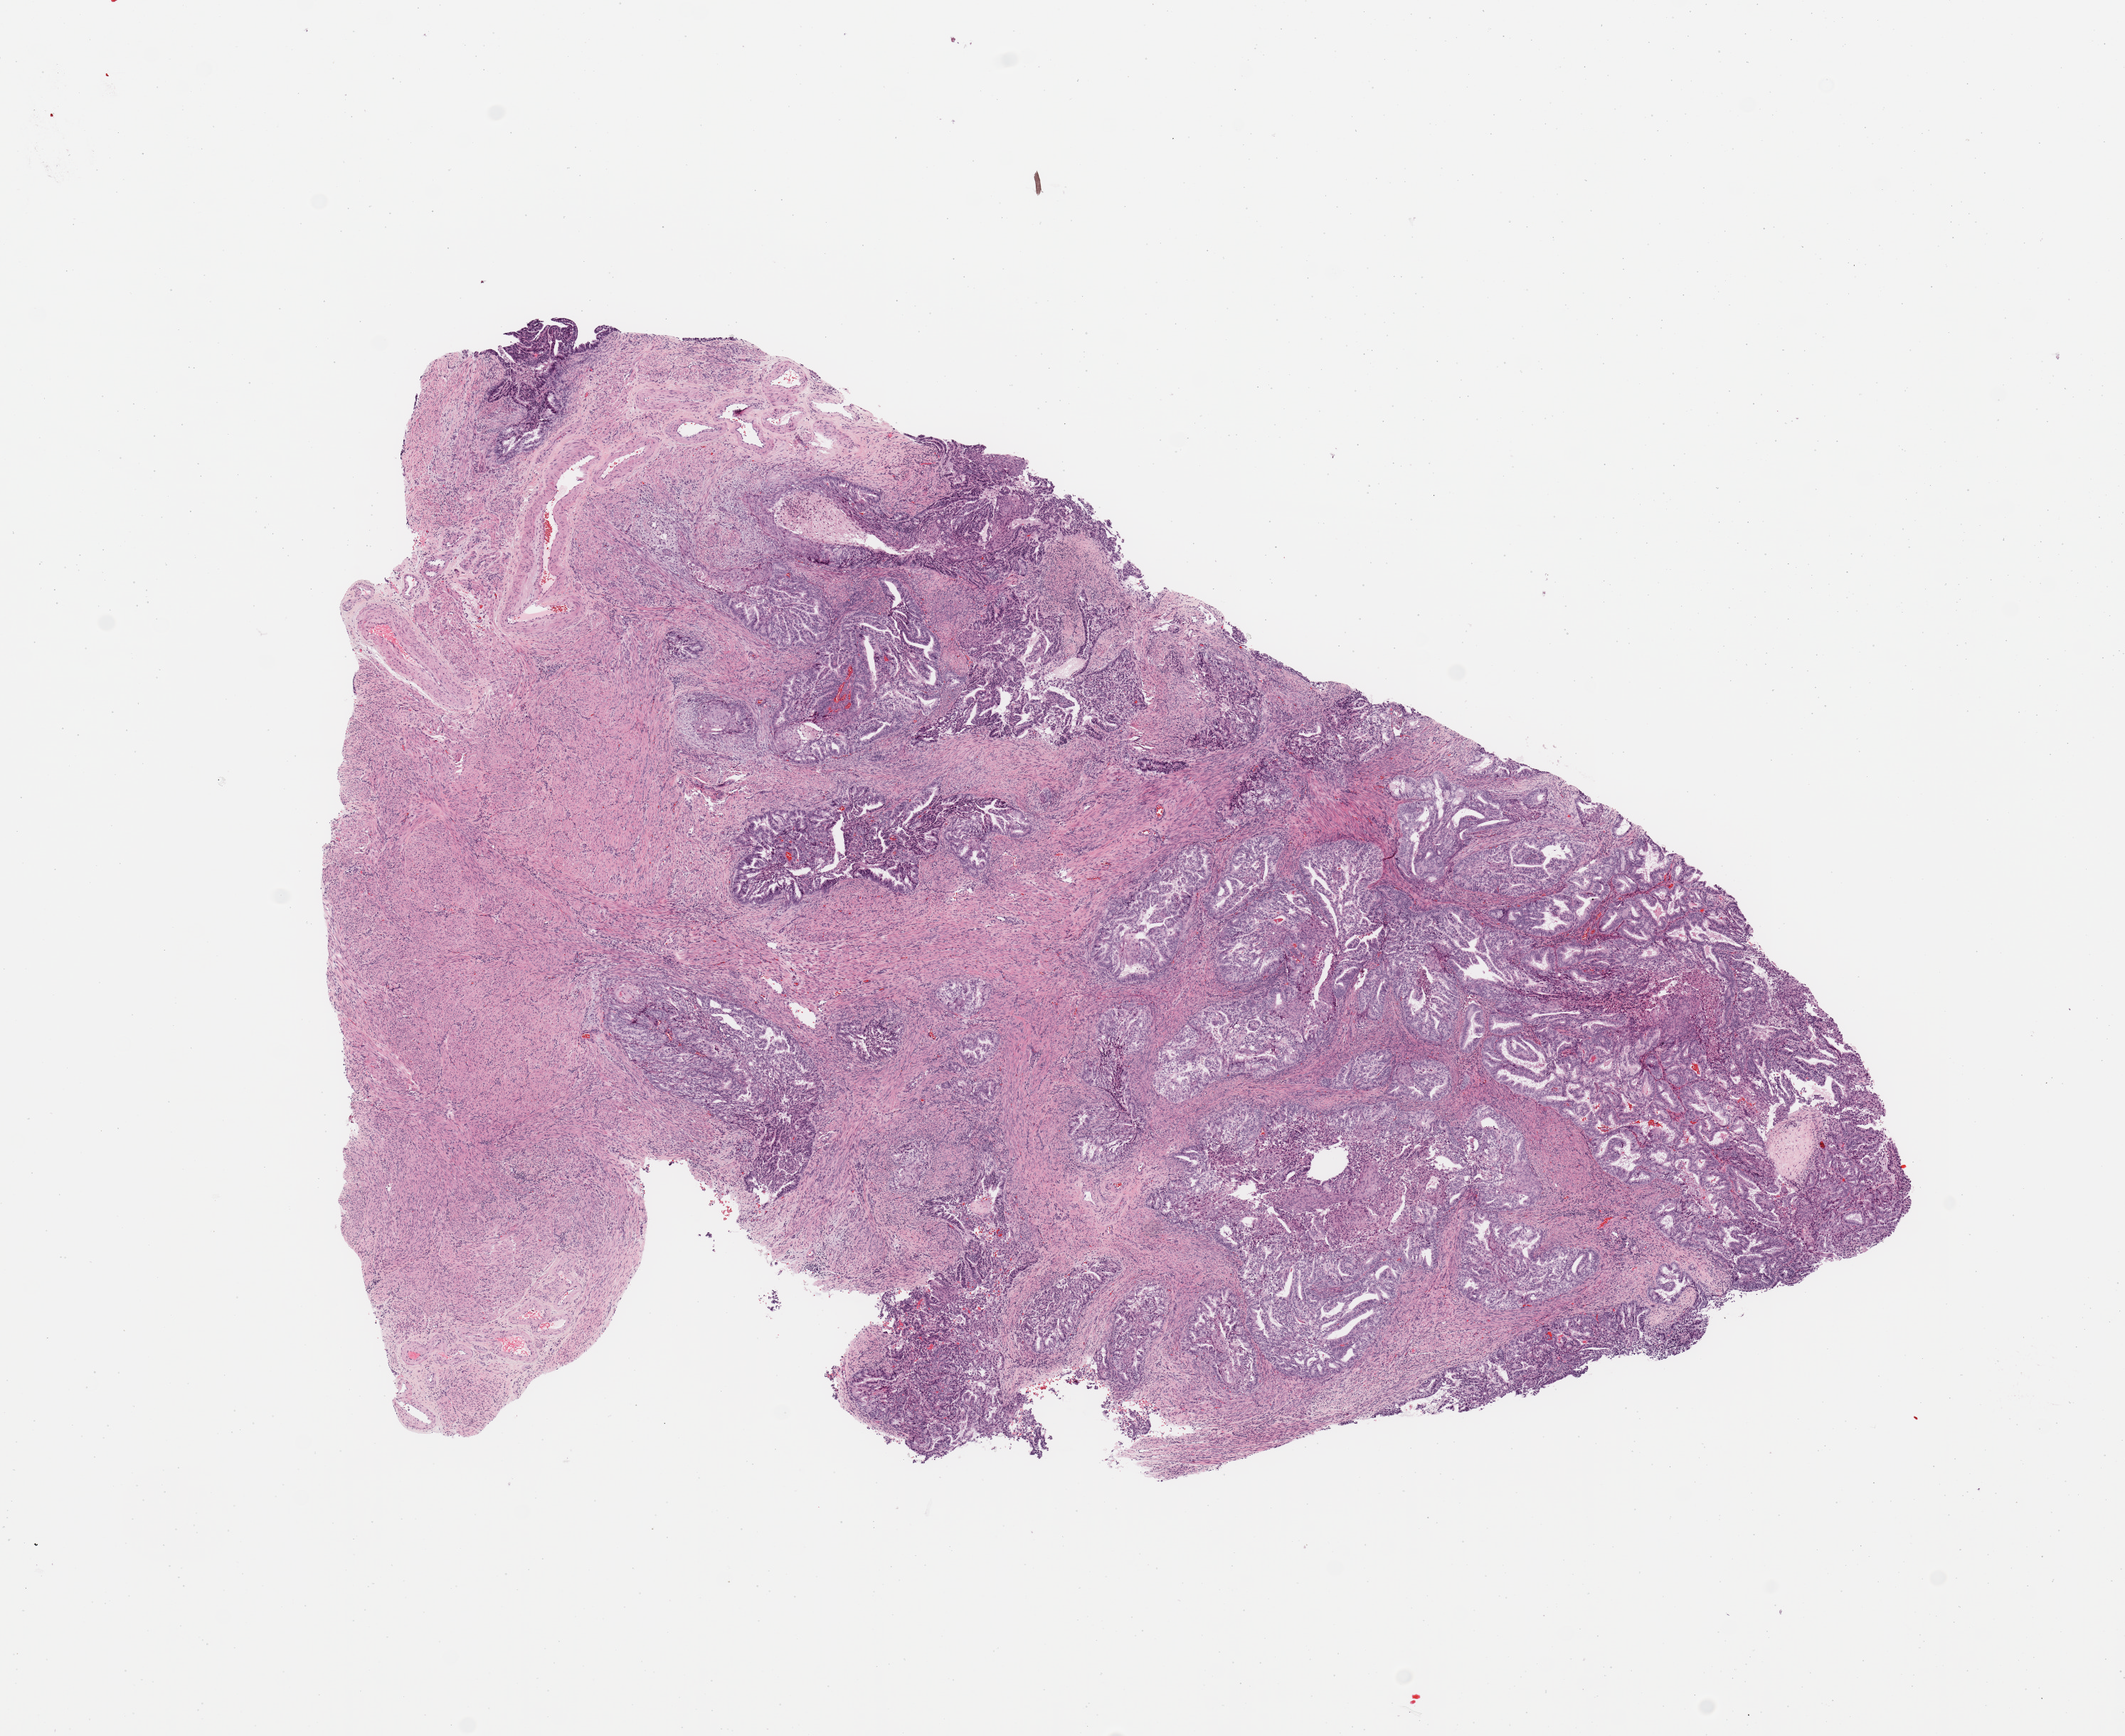
H&E whole-slide image, a low-resolution overview of the entire scanned area, about 11.8 x 9.6 mm; uterus, normal (non-tumour) tissue. Patient: female, age 59 years.
- this section: normal (non-tumour) tissue from the same patient
- patient diagnosis: Endometrioid adenocarcinoma, NOS